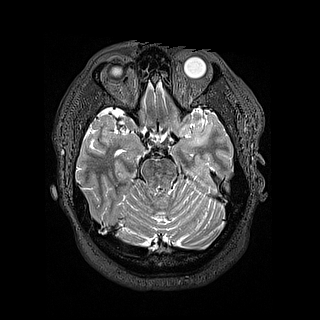
Brain MRI from a brain-tumour surgery series, one axial slice; slice 103 of 144 in the series (ordered by position); 1.2 mm slice thickness; 320 × 320 image matrix, field of view 254 × 254 mm. Case-level facts recorded for this patient, not image findings: histopathology: Astrocytoma; WHO grade: 2; IDH mutation: yes.
Annotated regions visible in this slice (outlined manually by an expert reader):
- tumour: bounding box [x1, y1, x2, y2] px = [186, 116, 203, 148]